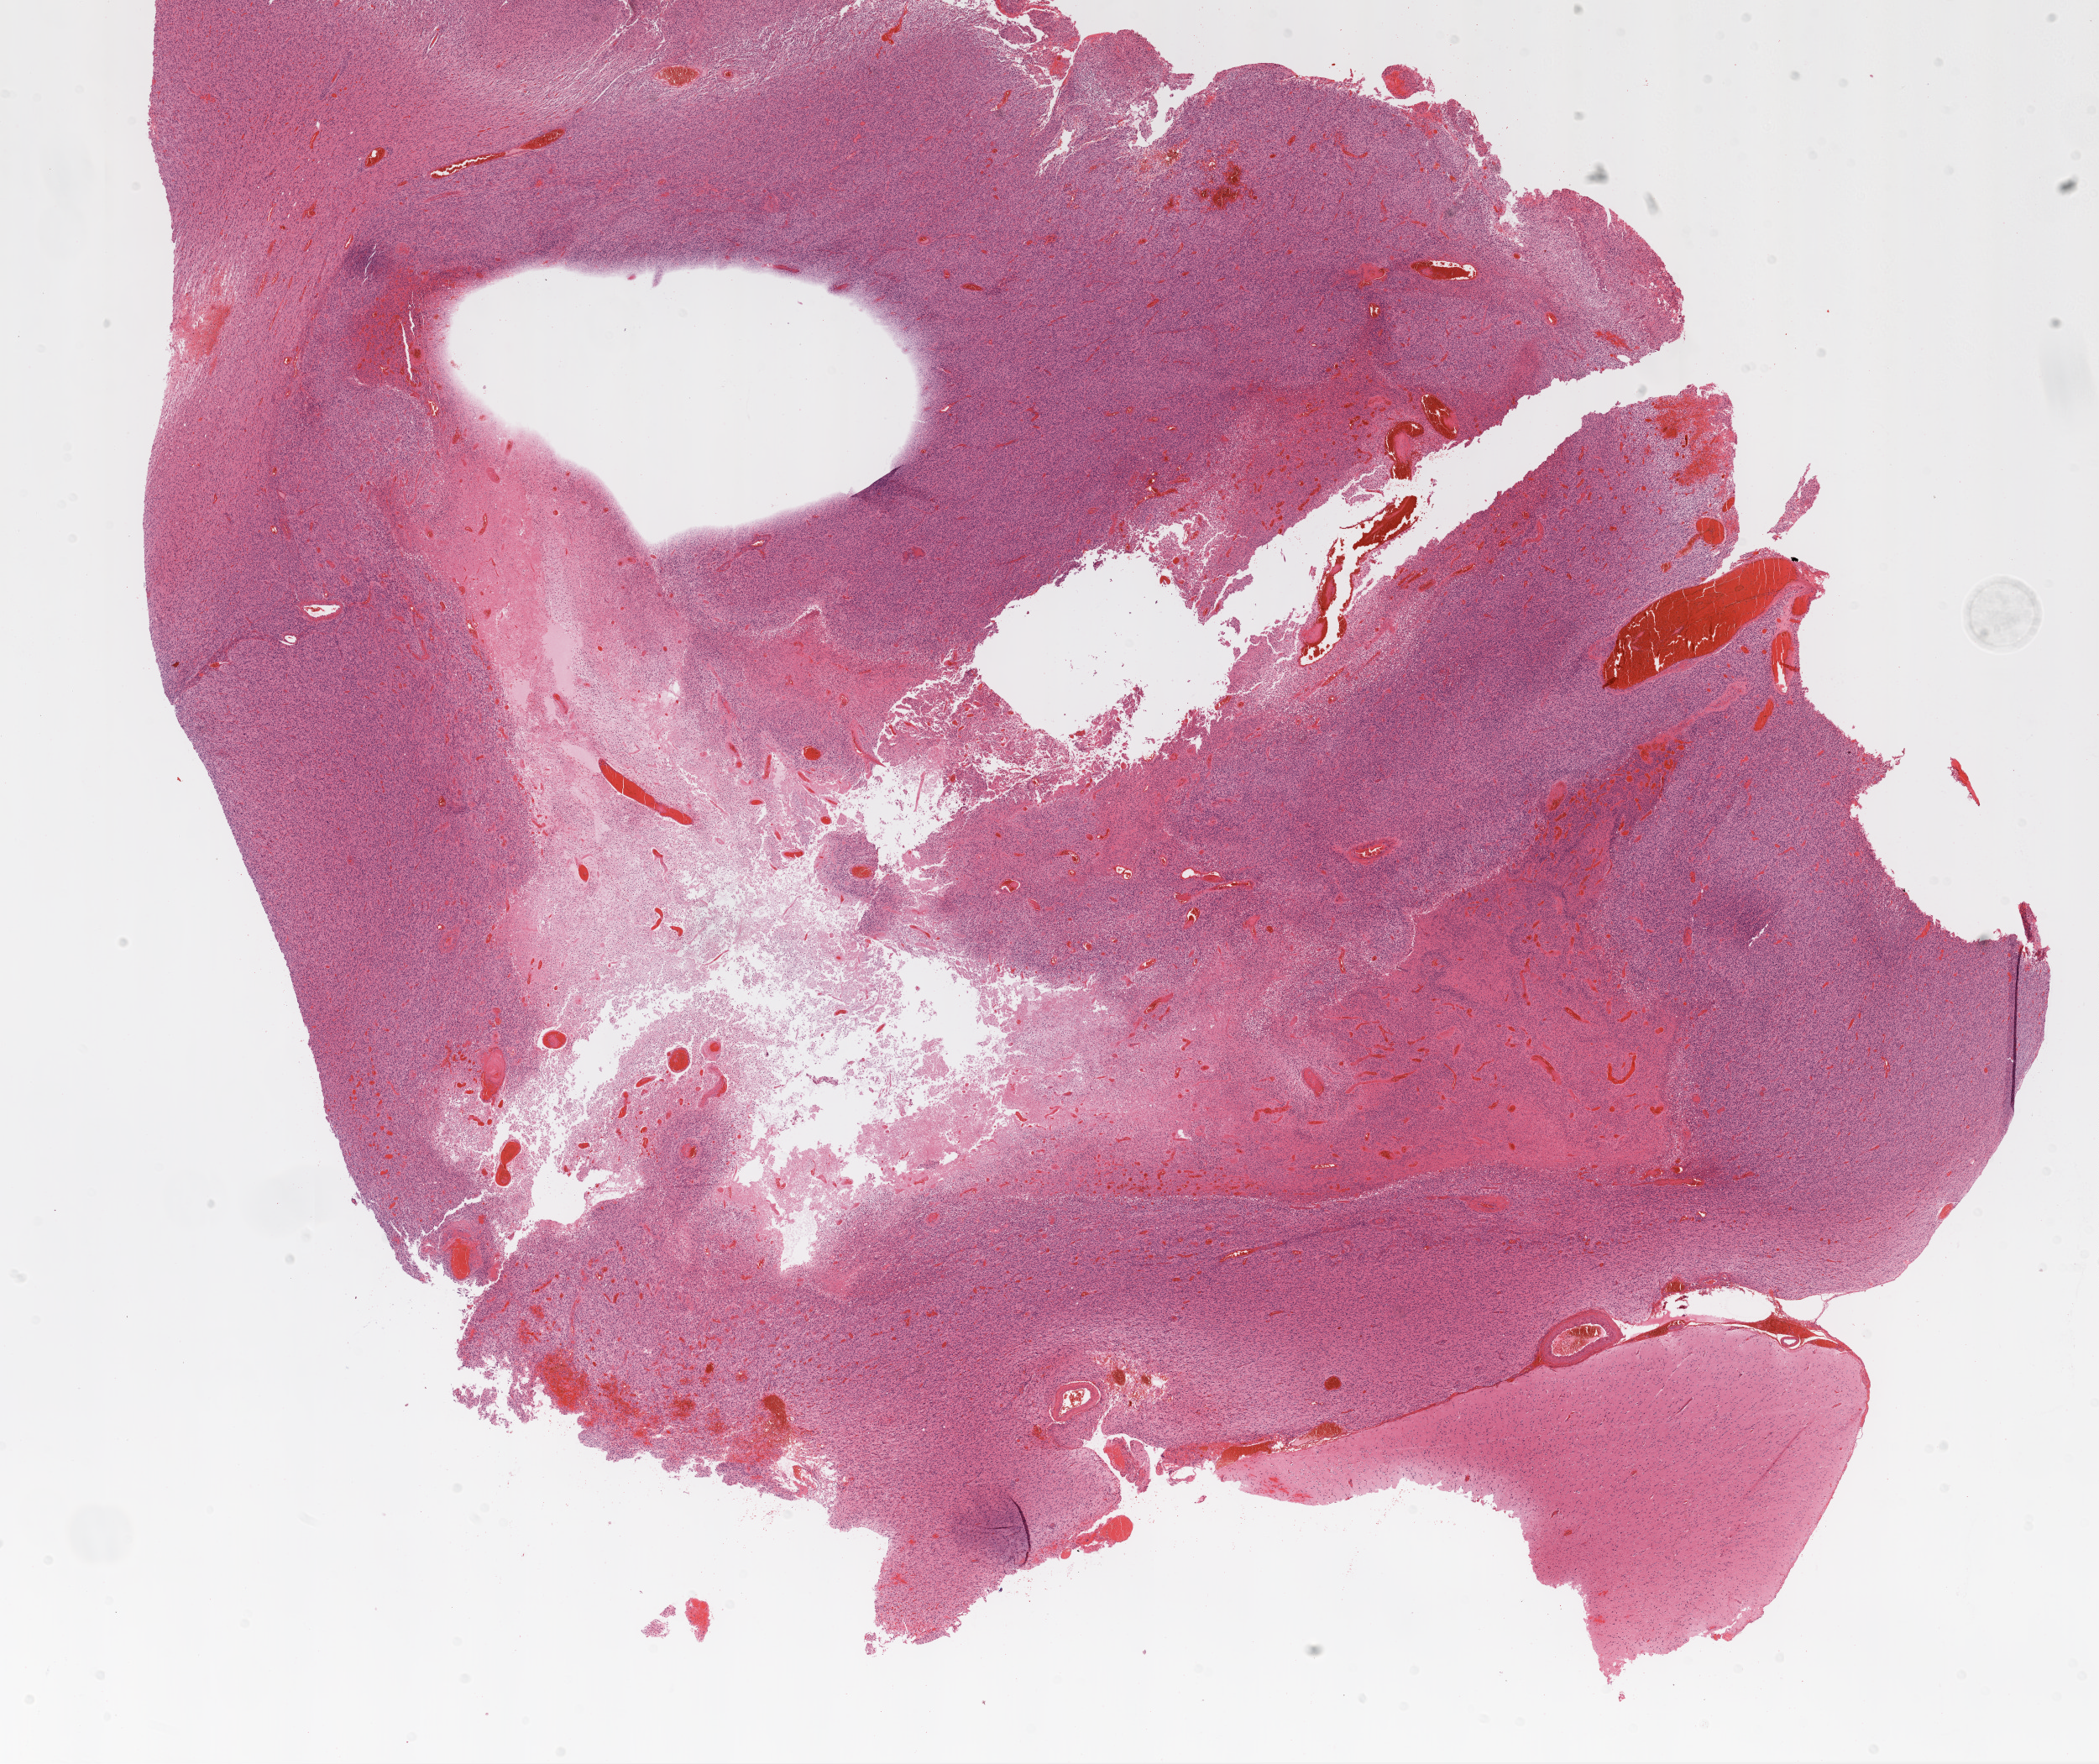
H&E whole-slide image, shown as a low-resolution overview of the whole scanned area (about 20.1 x 16.9 mm, acquisition: 20x scan); formalin-fixed paraffin-embedded (FFPE) diagnostic section; primary tumour sample from the brain. Female patient; age at initial diagnosis 63 years.
Diagnosis: Glioblastoma.